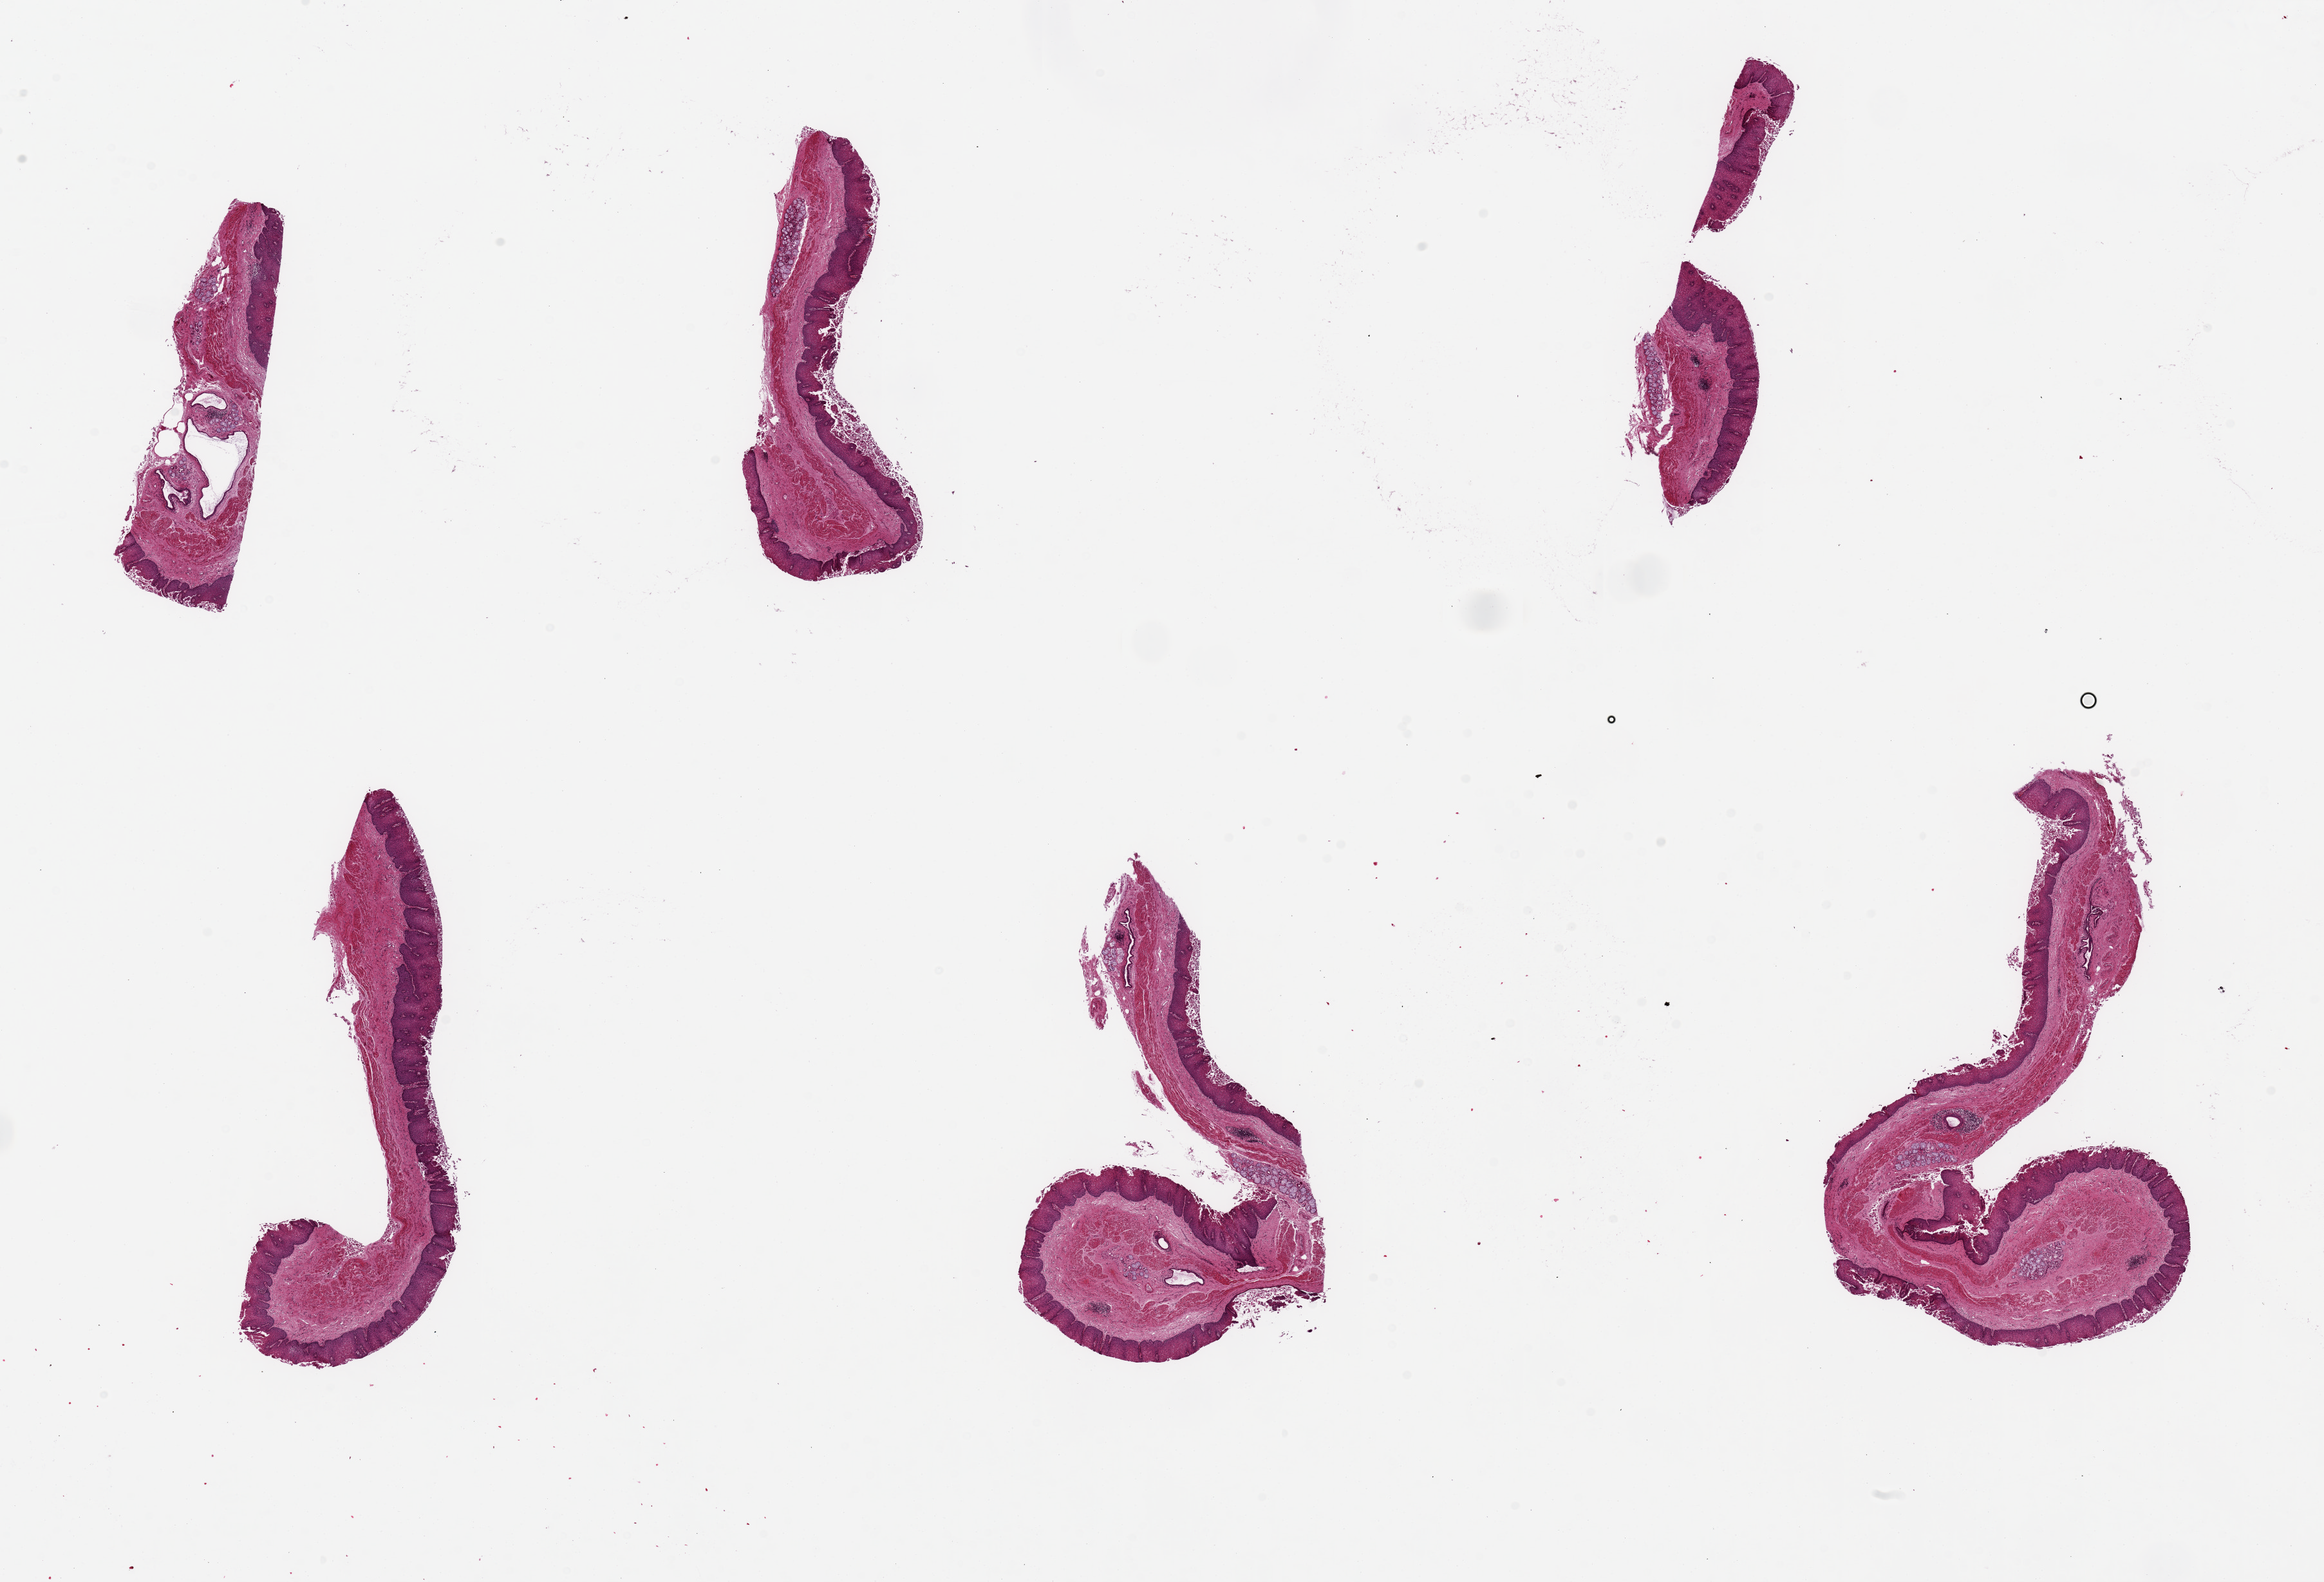
Digitized hematoxylin and eosin (H&E)-stained section, brightfield — shown as a low-resolution overview of the whole scanned area (about 28.5 x 19.4 mm); PAXgene-fixed paraffin-embedded (PFPE) section; target tissue: esophageal mucous membrane; tissue donor sample. Donor: male.
* review note (as recorded): 6 pieces, up to 7x4mm; squamous epithelium is ~40% thickness